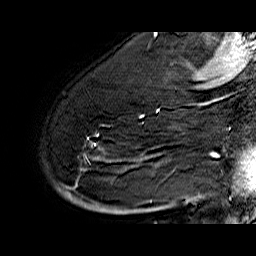
Breast MRI (dynamic contrast-enhanced), one sagittal slice; position 45 of 60 along the scan axis; dynamic contrast-enhanced series, time point 2 of 6 at this slice position (early post-contrast); 1.5 T; TE 6.4 ms, TR 32.9 ms; 256 × 256 image matrix, field of view 200 × 200 mm. Female patient. From the clinical record (not read from this slice): setting: breast cancer imaged before/during neoadjuvant chemotherapy; receptor status: HR-positive, HER2-negative.
Outlined on this slice (semi-automatic segmentation, software-assisted and operator-edited):
- analysis volume of interest (the breast-tissue region the enhancement analysis was run in; not a lesion): bounding box [x1, y1, x2, y2] px = [53, 74, 176, 210]
- tumour enhancement mask (voxels above the 100 % enhancement threshold inside the analysis volume of interest): [58, 109, 158, 202]